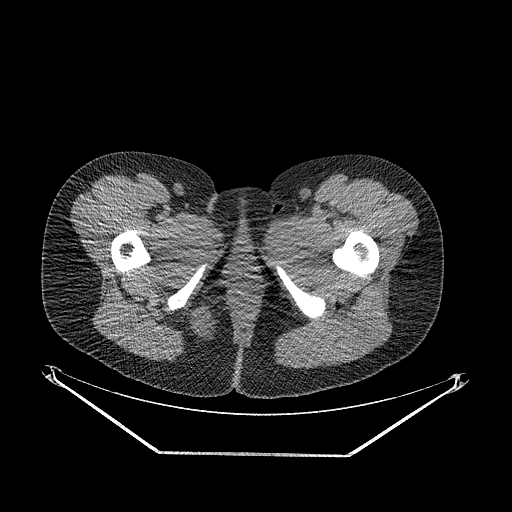
CT of an extremity soft-tissue mass (from a PET/CT study), one axial slice. Slice 32 of 267 in the series (ordered by position). Reconstruction kernel STANDARD. Soft-tissue window (W 400 / L 40 HU). 3.75 mm slice thickness. 512 × 512 image matrix, field of view 500 × 500 mm. Female patient. From the clinical record (not read from this slice): histological type: epithelioid sarcoma; grade: intermediate; site of the primary tumour: right buttock.
Structures marked on this image (expert contour drawn on MRI and transferred to this co-registered scan by the dataset authors):
- gross tumour volume including surrounding oedema: box from (x=178, y=297) to (x=222, y=348) px
- gross tumour volume (mass): (x=181, y=306)–(x=215, y=343)